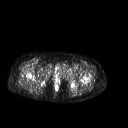
FDG PET of an extremity soft-tissue mass (from a PET/CT study), one axial slice; slice 258 of 267 in the series (ordered by position); 3.27 mm slice thickness; 128 × 128 image matrix, field of view 500 × 500 mm. Female patient, age 42 years. Case-level facts recorded for this patient, not image findings: histological type: pleiomorphic leiomyosarcoma; grade: intermediate; site of the primary tumour: left thigh.
Outlined on this slice (expert contour drawn on MRI and transferred to this co-registered scan by the dataset authors):
- gross tumour volume including surrounding oedema: bounding box <61,66,68,70> (left, top, right, bottom; pixels)